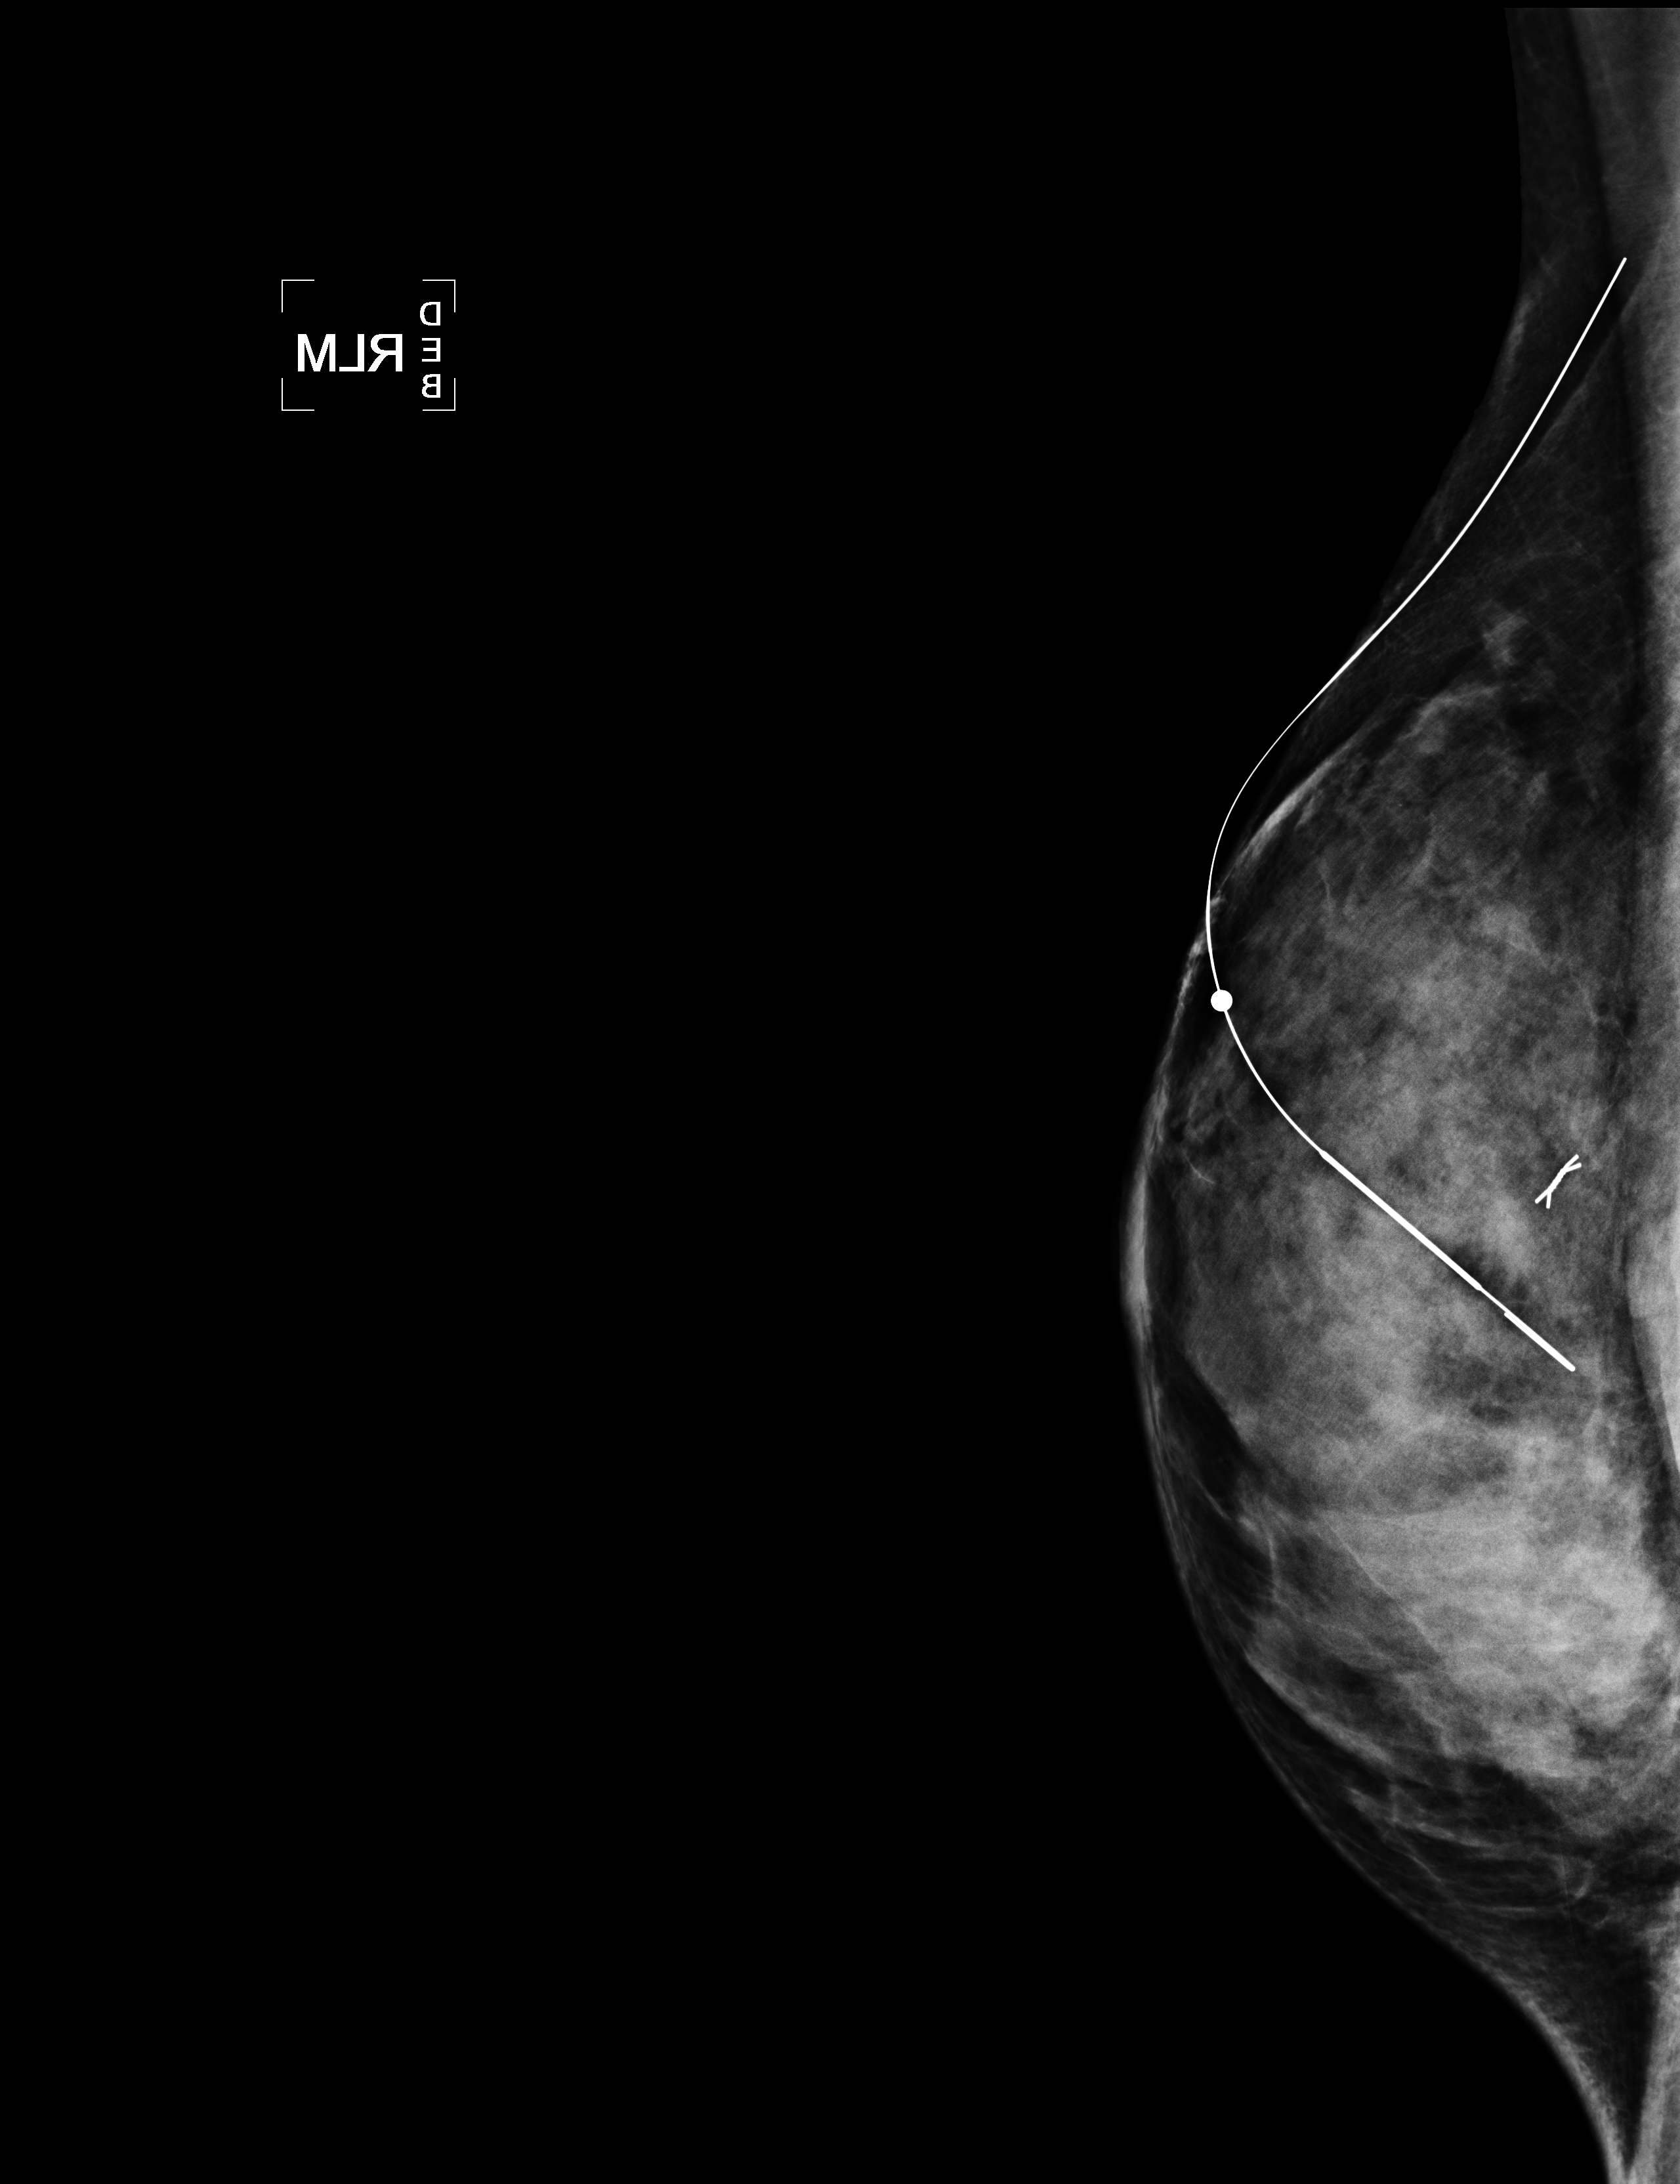
Mammogram, right breast, LM view; patient in her 20s.
Patient-level pathology facts (clinical record, not image findings): pathology diagnosis: Invasive ductal carcinoma, modified Scarff-Bloom-Richardson grade II/III. No intraductal carcinoma component seen. (right breast); receptor status (as recorded): ER pos (strong), PR pos (strong), HER2 neg (weak); Ki-67 (as recorded): pos (strong); clinical background (as recorded): late 20's y.o. with bx-proven CA.